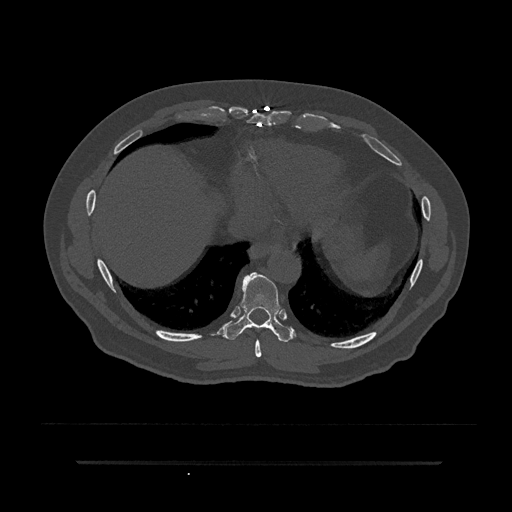
CT including the spine, one axial slice. Position 388 of 797 along the scan axis. 120 kVp. Bone window (W 1800 / L 400 HU). 512 × 512 image matrix, field of view 464 × 464 mm. Patient: male, 59 years. From the clinical record (not read from this slice): primary cancer: bile ducts.
Structures marked on this image (semi-automatic segmentation, software-assisted and operator-edited):
- T8 vertebra: bounding box <255,339,262,357> (left, top, right, bottom; pixels)
- T9 vertebra: <225,272,292,342>